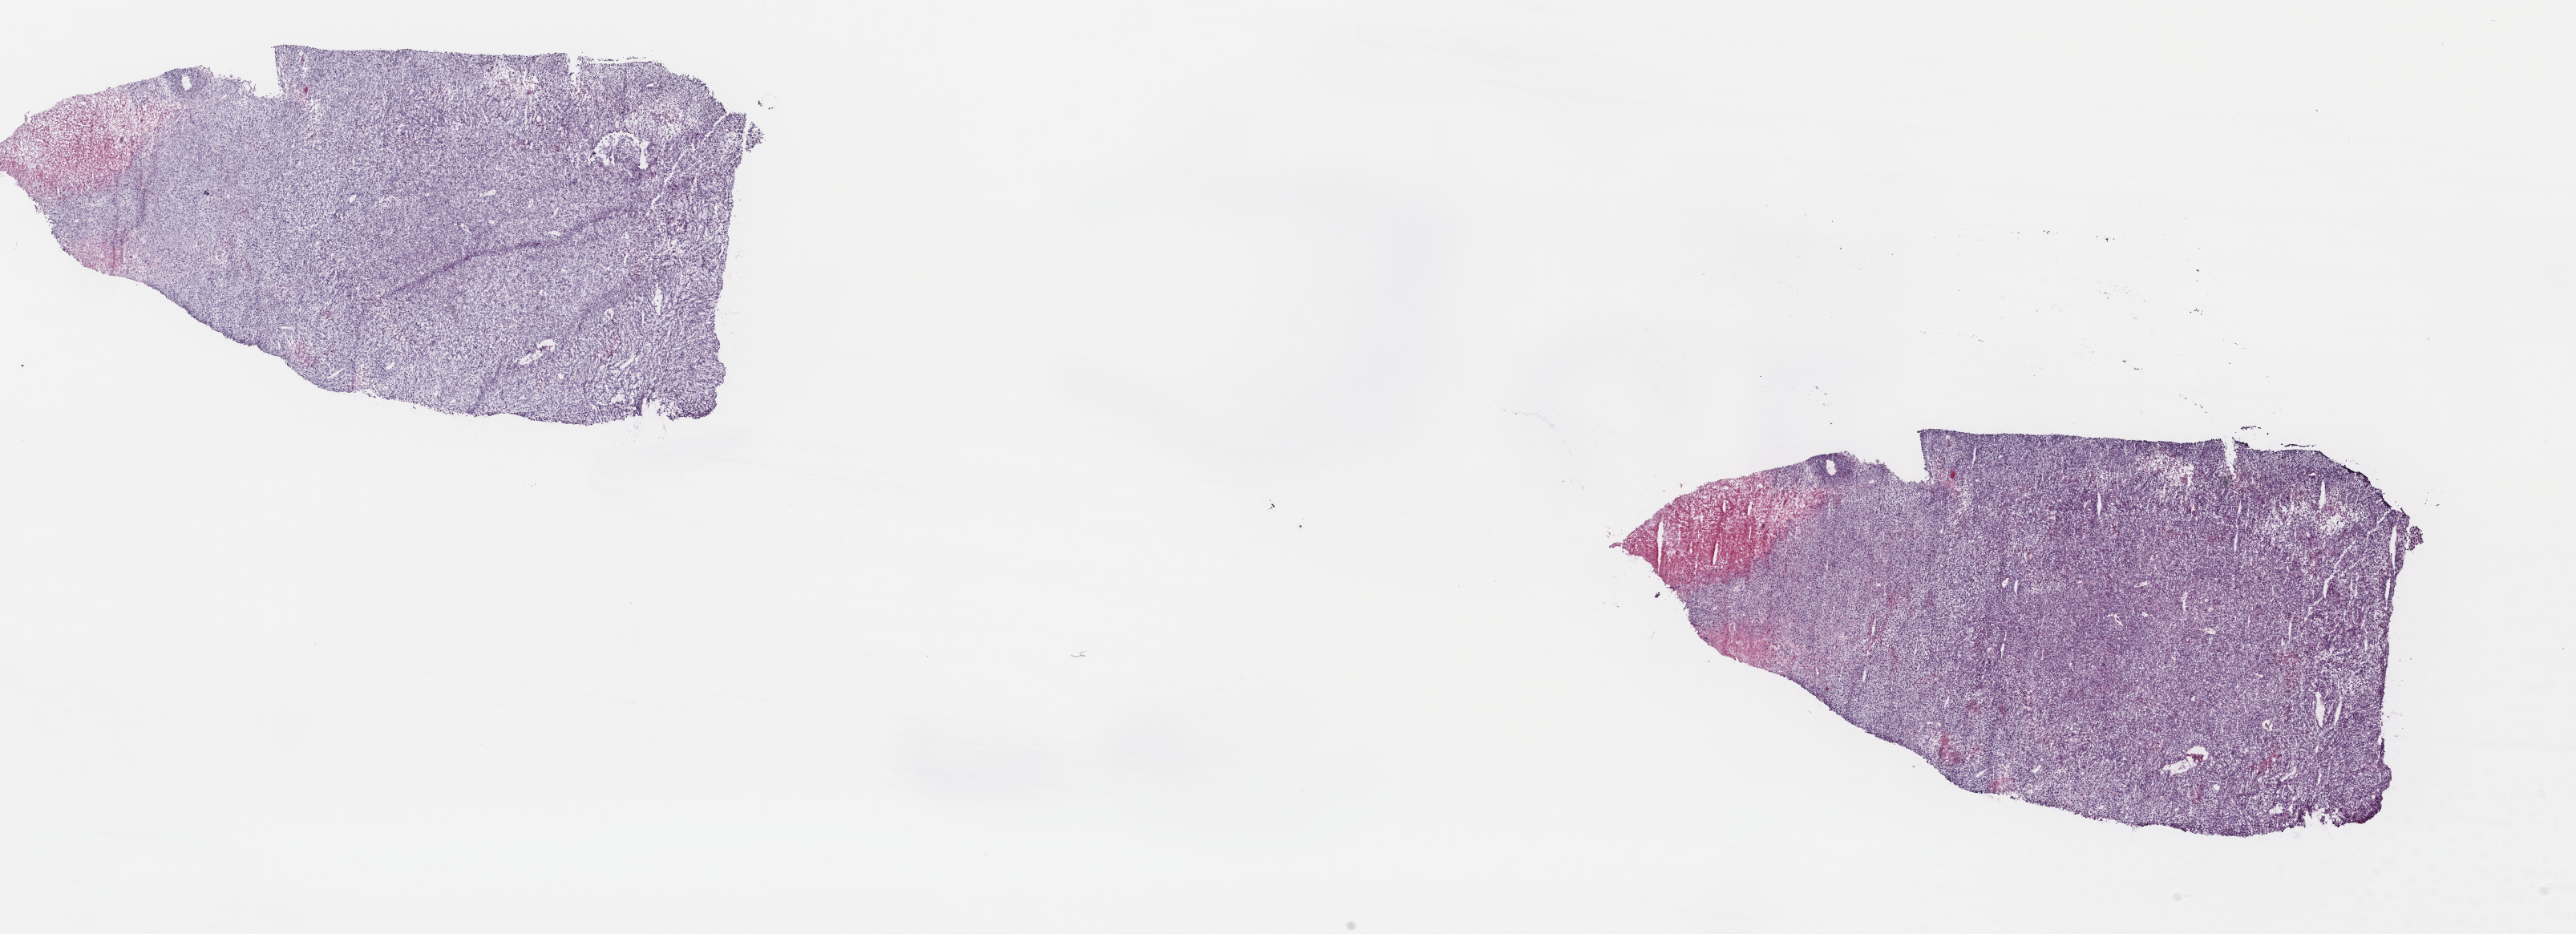
H&E whole-slide image, a low-resolution overview of the entire scanned area, about 25.3 x 9.2 mm (slide scanned at 40x). Frozen section. Uterus, primary tumour sample. Female, age 72 years at initial diagnosis. Slide review estimates, as recorded: tumour cells 85%, tumour nuclei 100%, normal cells 0%, stromal cells 5%, necrosis 10%. Inflammatory infiltration, as recorded: lymphocyte infiltration 0%, monocyte infiltration 0%, neutrophil infiltration 0%.
FIGO stage: IVB. Histologic diagnosis: Mullerian mixed tumor.